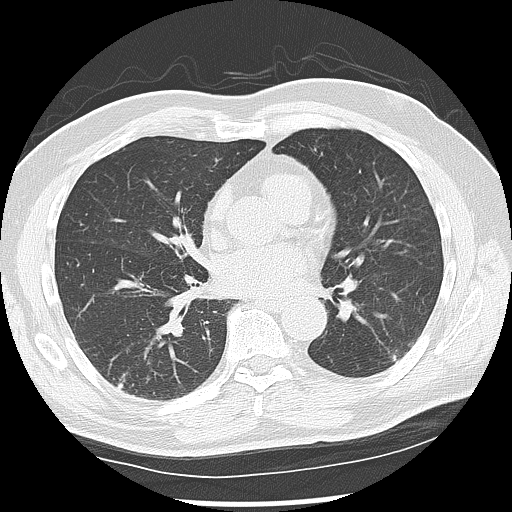
Low-dose screening chest CT, one axial slice. Slice 62 of 142 in the series (ordered by position). Reconstruction kernel LUNG. 120 kVp. Lung window (W 1500 / L -600 HU). 2.5 mm slice thickness. 512 × 512 image matrix, field of view 360 × 360 mm.
Structures marked on this image (manually delineated by an expert):
- lesion 1 (nodule, lower lobe of left lung): box from (x=392, y=350) to (x=401, y=362) px